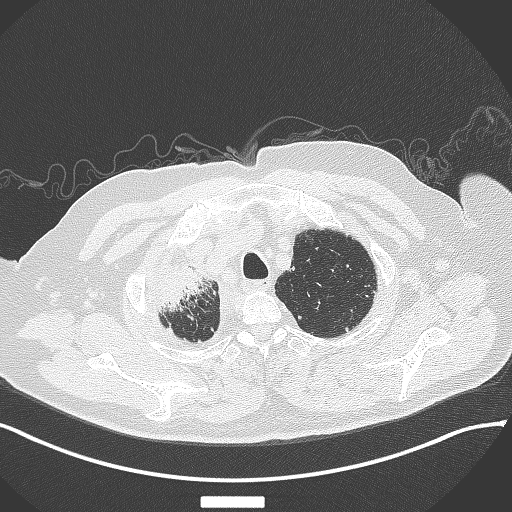
Chest CT, one axial slice; slice 322 of 384 in the series (ordered by position); reconstruction kernel B70f; 120 kVp; lung window (W 1500 / L -600 HU); 1 mm slice thickness; 512 × 512 image matrix, field of view 400 × 400 mm. Male patient, age 69 years. Case-level facts recorded for this patient, not image findings: clinical TNM (as recorded): T4 N3 M1.
Annotated regions visible in this slice (bounding box drawn by a radiologist):
- lung tumour (recorded histology: adenocarcinoma): bounding box <151,259,217,323> (left, top, right, bottom; pixels)